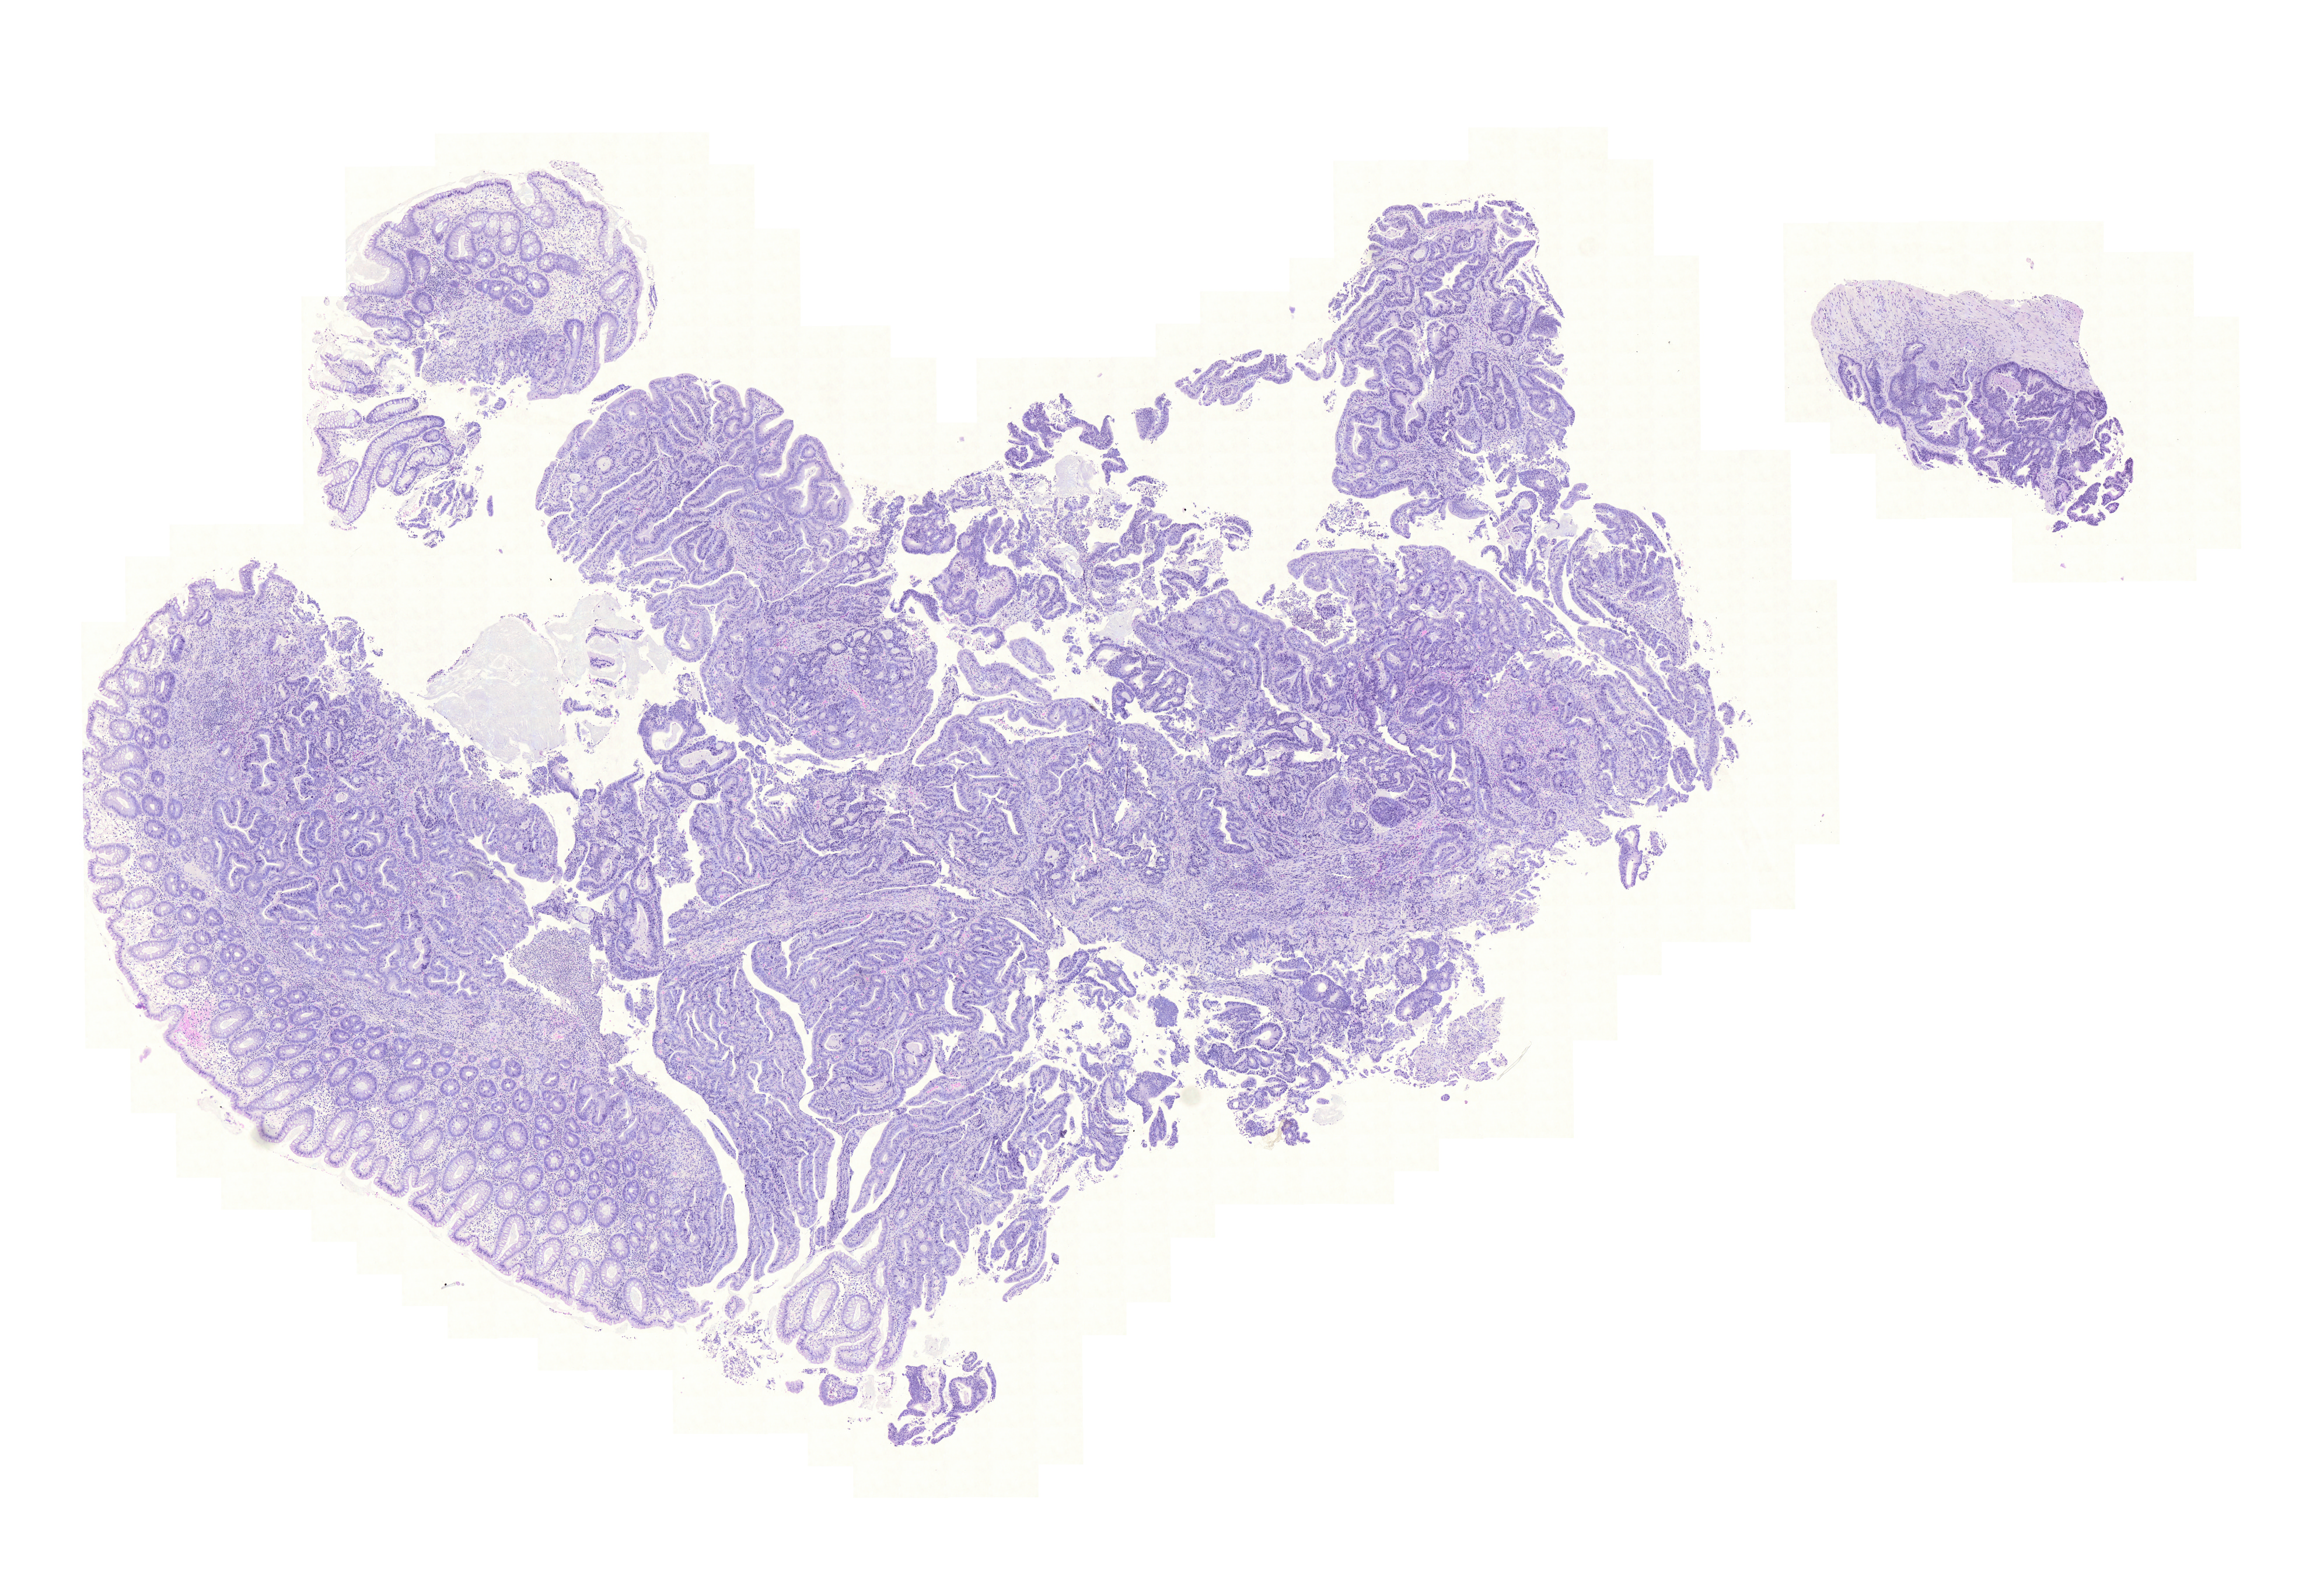
Digitized H&E-stained tissue section (whole slide) — shown as a low-resolution overview of the whole scanned area (about 14.7 x 10.2 mm); FFPE section; sample: primary tumour, colon. Female, age 57 years at initial diagnosis.
• TNM: T3 N0 M0
• AJCC pathologic stage: IIA (6th edition)
• lymph nodes positive (case pathology): 0 of 18 examined
• pathologic diagnosis: Adenocarcinoma, NOS (sigmoid colon)